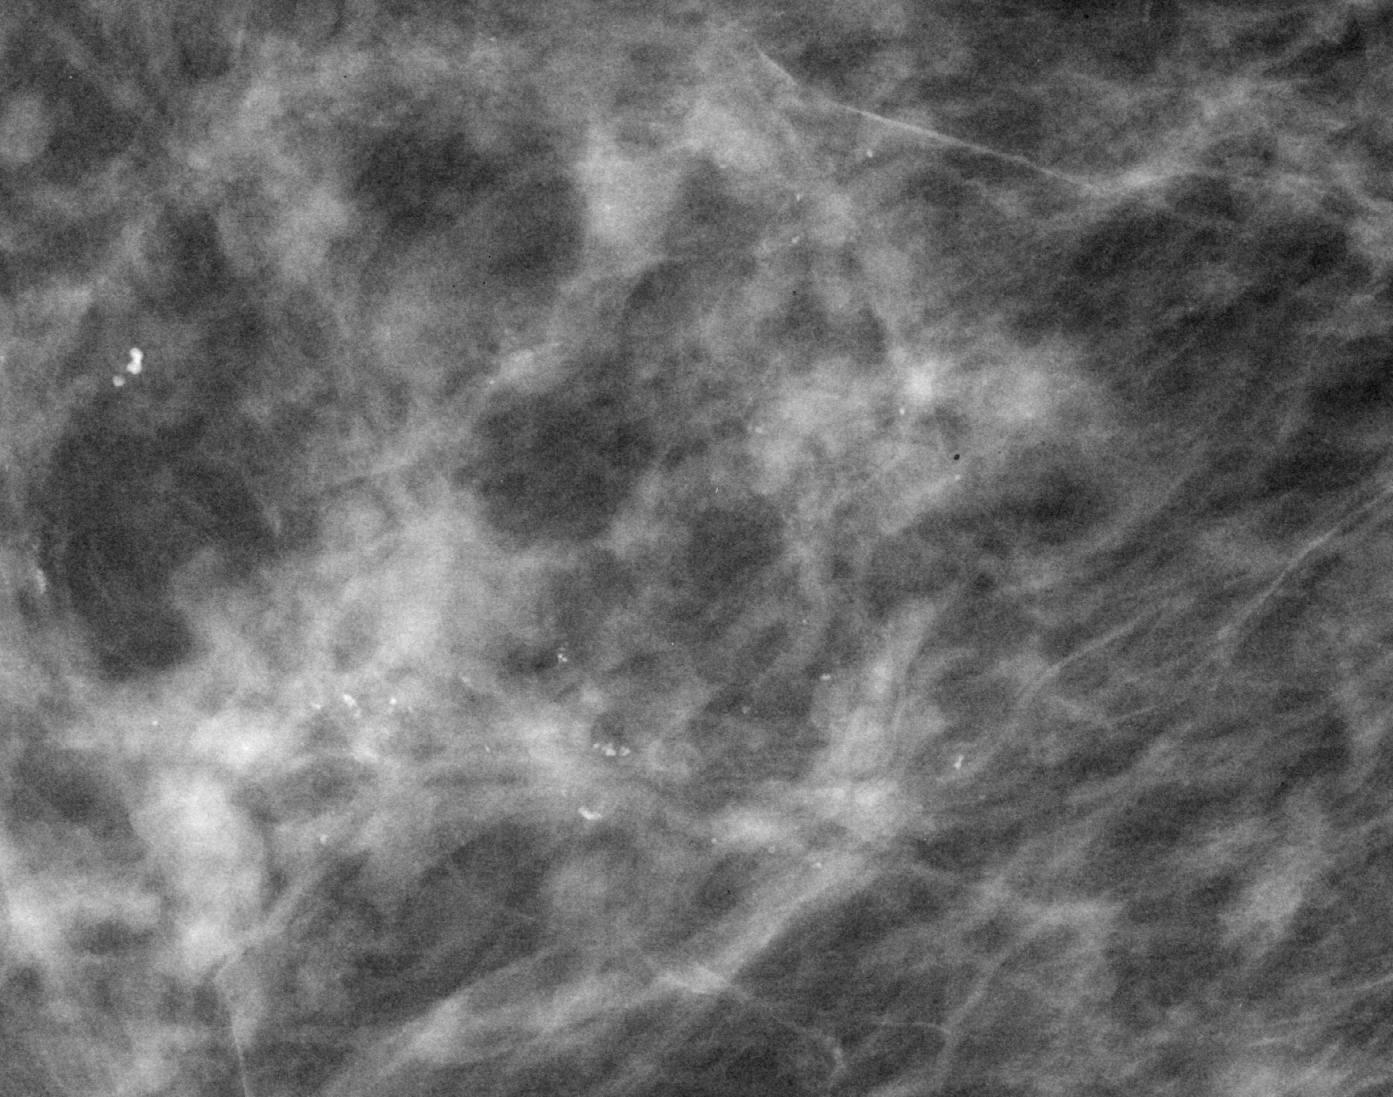
Cropped region of a digitized screen-film mammogram centred on a radiologist-marked abnormality; right breast; MLO view.
- Calcifications, morphology pleomorphic, distribution segmental; BI-RADS assessment category 4; pathology result (as recorded, not read from the image): malignant.